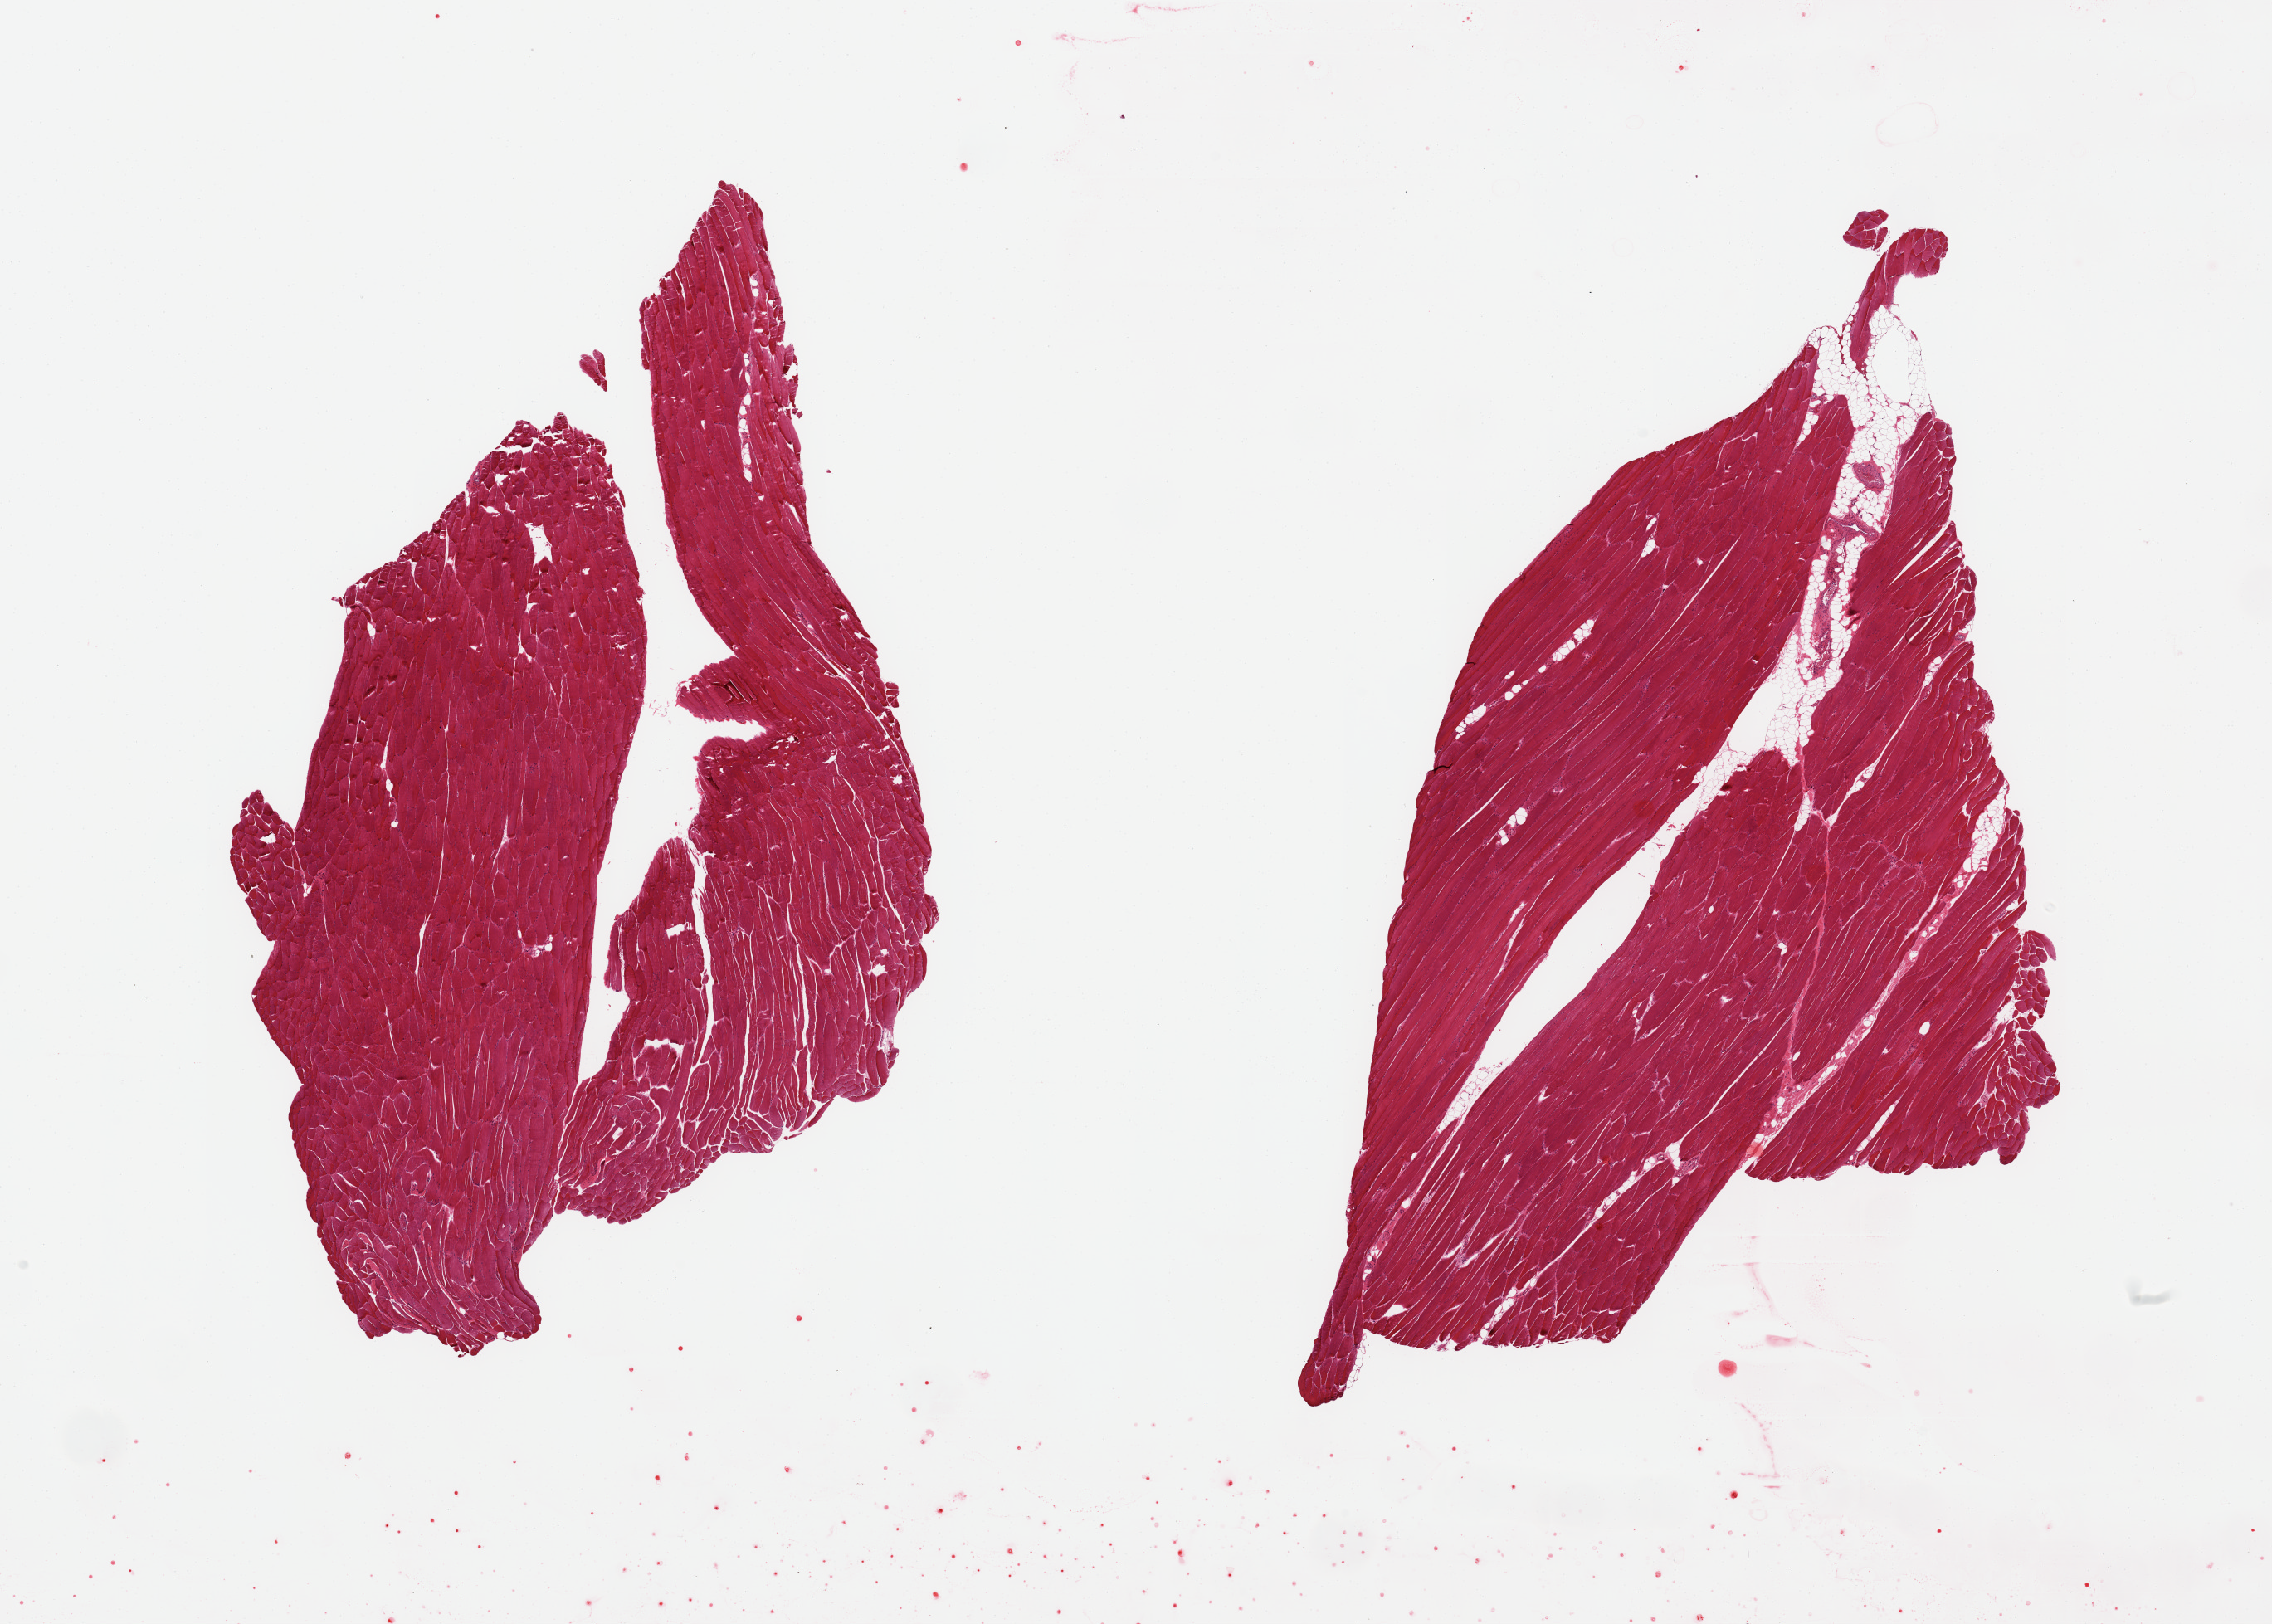
Haematoxylin and eosin whole-slide image, a low-resolution overview of the entire scanned area, about 21.7 x 15.5 mm. PAXgene-fixed, paraffin-embedded tissue. Section of skeletal muscle (target tissue). Donor tissue sample. Donor sex: male.
* pathologist's review note for this sample: 2 pieces, ~10% interstitial fat